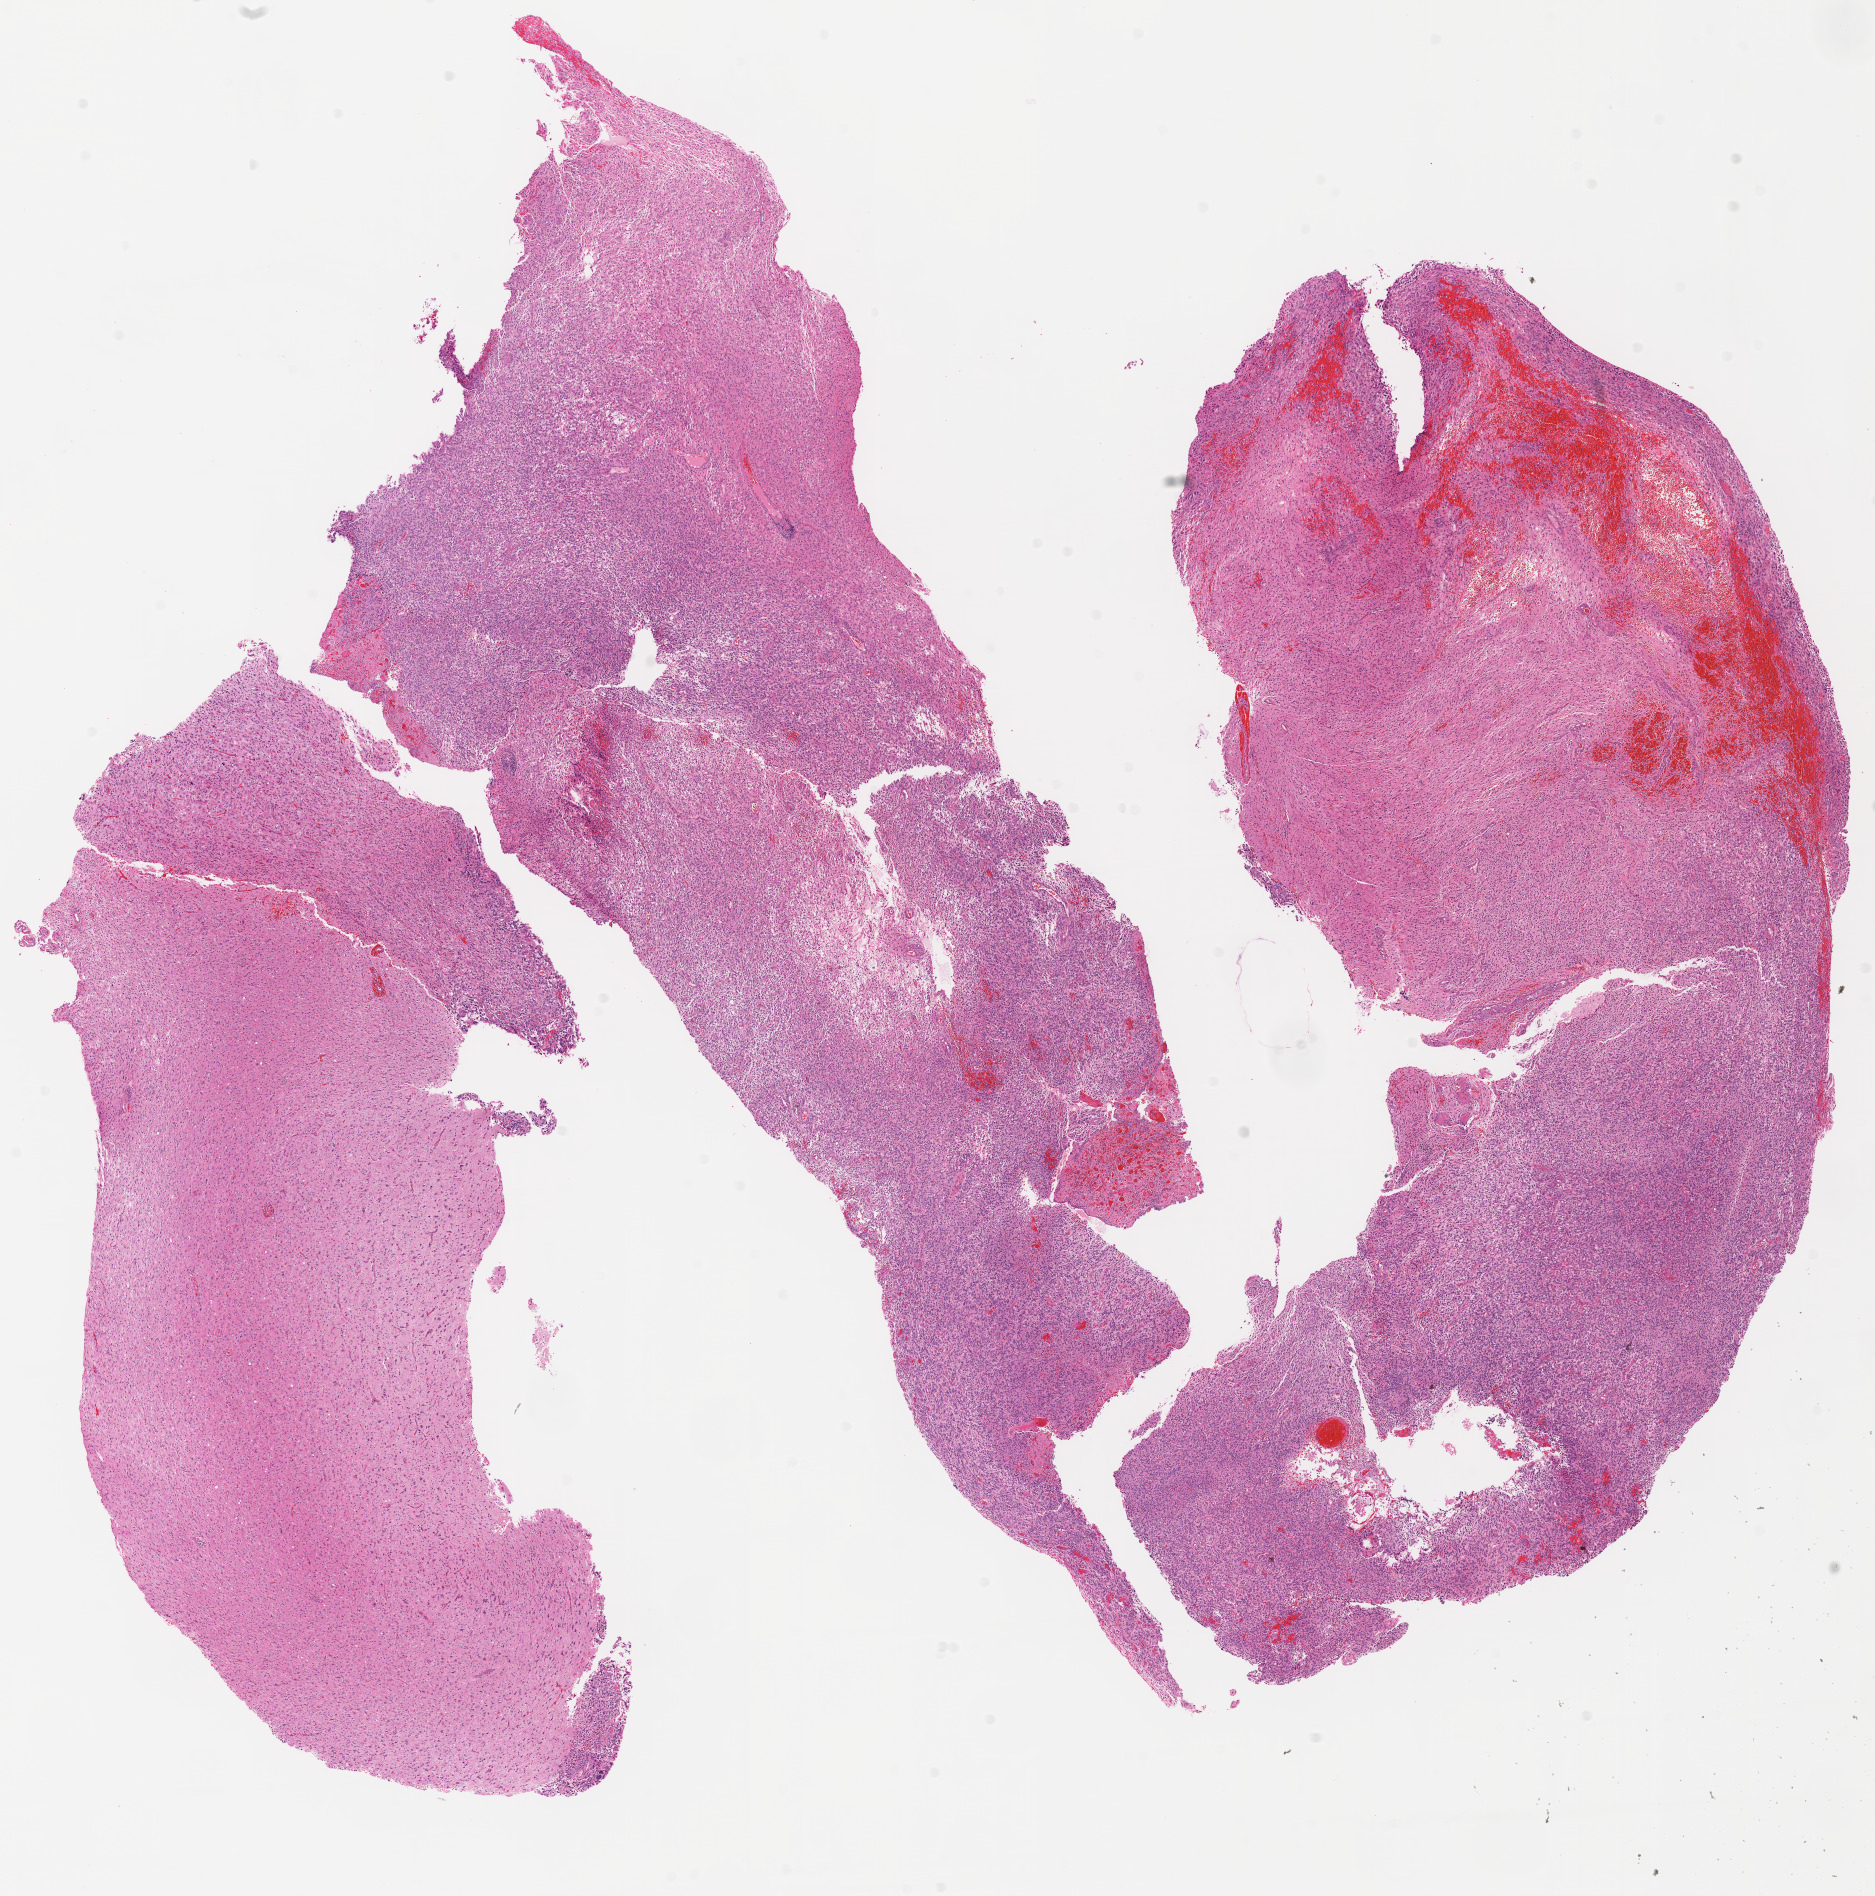
Hematoxylin and eosin (H&E) stained whole-slide image, low-resolution overview of the scanned area, about 15.0 x 15.2 mm (acquisition: 20x scan). Formalin-fixed paraffin-embedded (FFPE) diagnostic section. Sample: primary tumour, brain. Female, age 42 years at initial diagnosis.
- histologic diagnosis: Glioblastoma